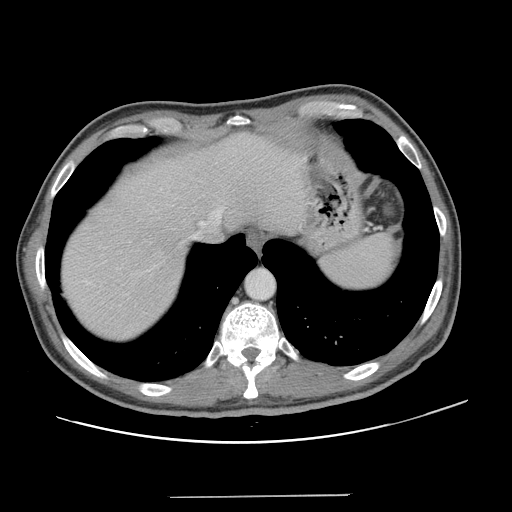
Contrast-enhanced abdominal CT, one axial slice; slice 113 of 131 in the series (ordered by position); soft-tissue window (W 400 / L 40 HU); 2.5 mm slice thickness; 512 × 512 image matrix, field of view 403 × 403 mm. Male patient, age 60 years. Case-level facts recorded for this patient, not image findings: diagnosis: colorectal cancer liver metastases, imaged before liver resection; multiple liver metastases: no; largest metastasis: 2.5 cm.
Structures marked on this image (expert manual segmentation):
- hepatic veins: box from (x=154, y=204) to (x=216, y=267) px
- liver: (x=62, y=134)–(x=302, y=341)
- planned liver remnant (the part of the liver to remain after resection): (x=62, y=134)–(x=302, y=337)